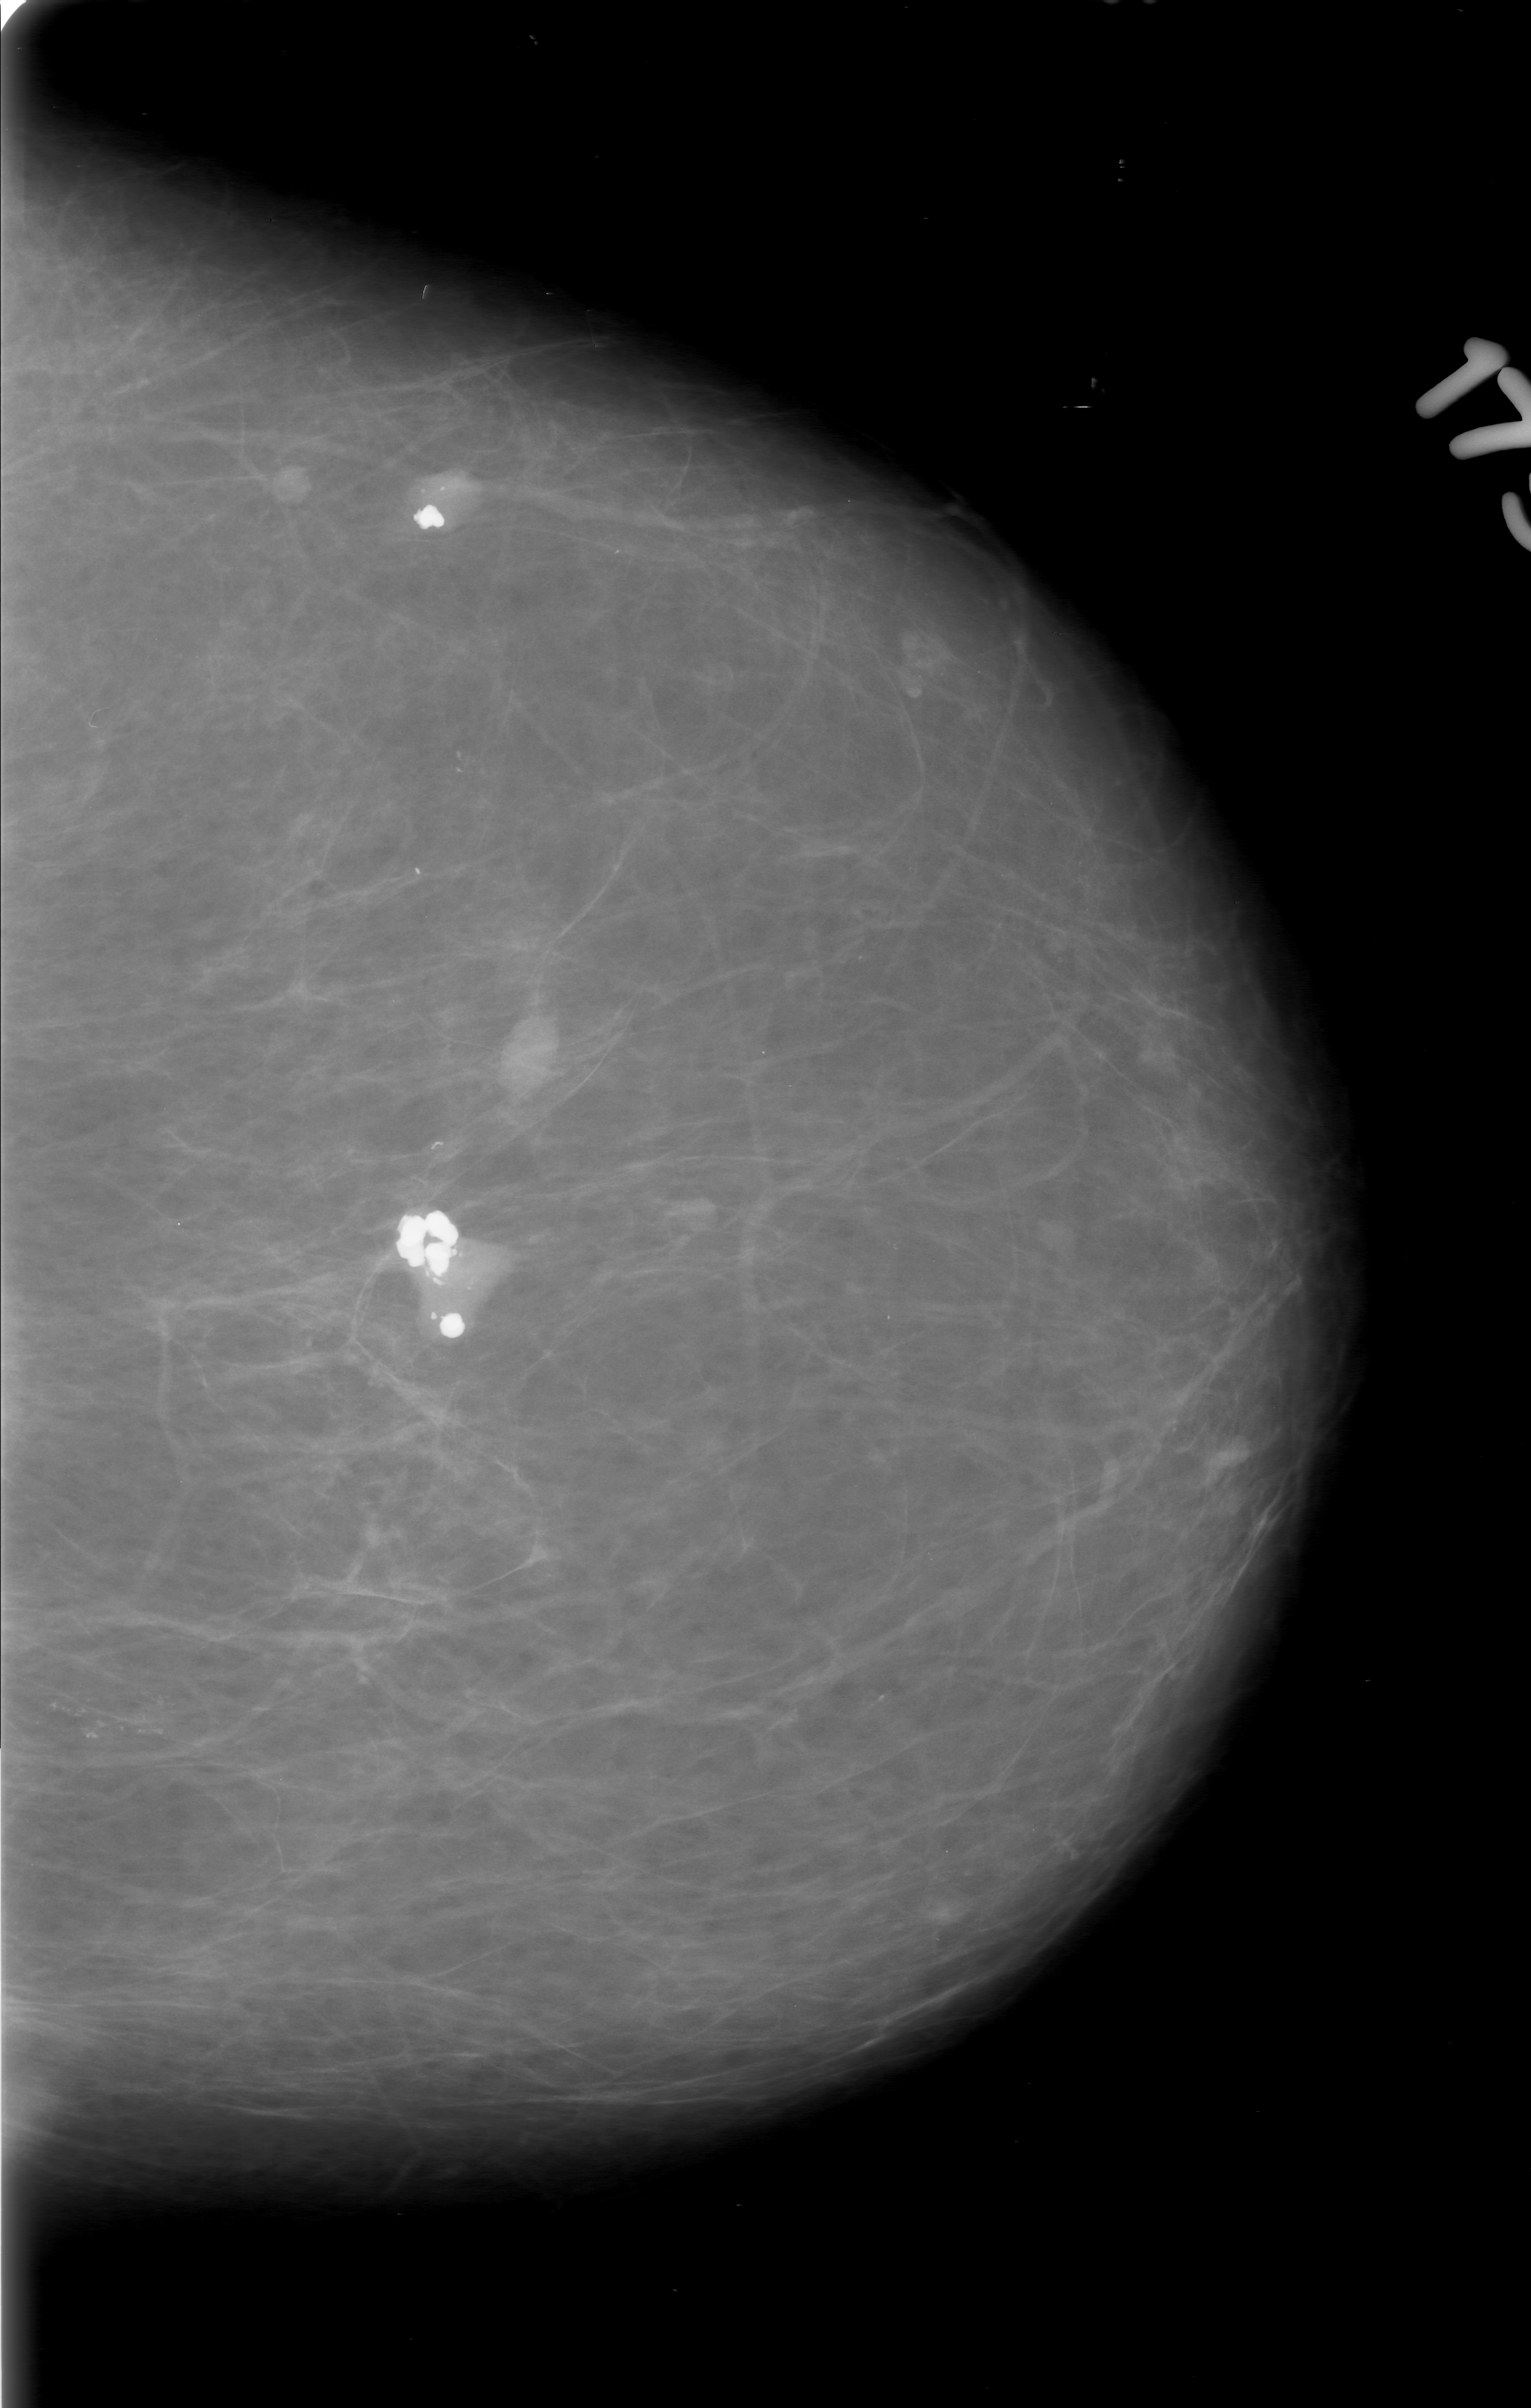
Mammogram (digitized film); left breast; CC view; breast composition: almost entirely fatty (BI-RADS density category 1 of 4); 1531 × 2408 image matrix.
Expert-marked regions of interest on this image (one box per marked abnormality):
- calcifications, morphology pleomorphic, distribution segmental; BI-RADS assessment category 0 (incomplete: needs additional imaging); pathology result (as recorded, not read from the image): benign: bounding box <6,1628,203,1812> (left, top, right, bottom; pixels)